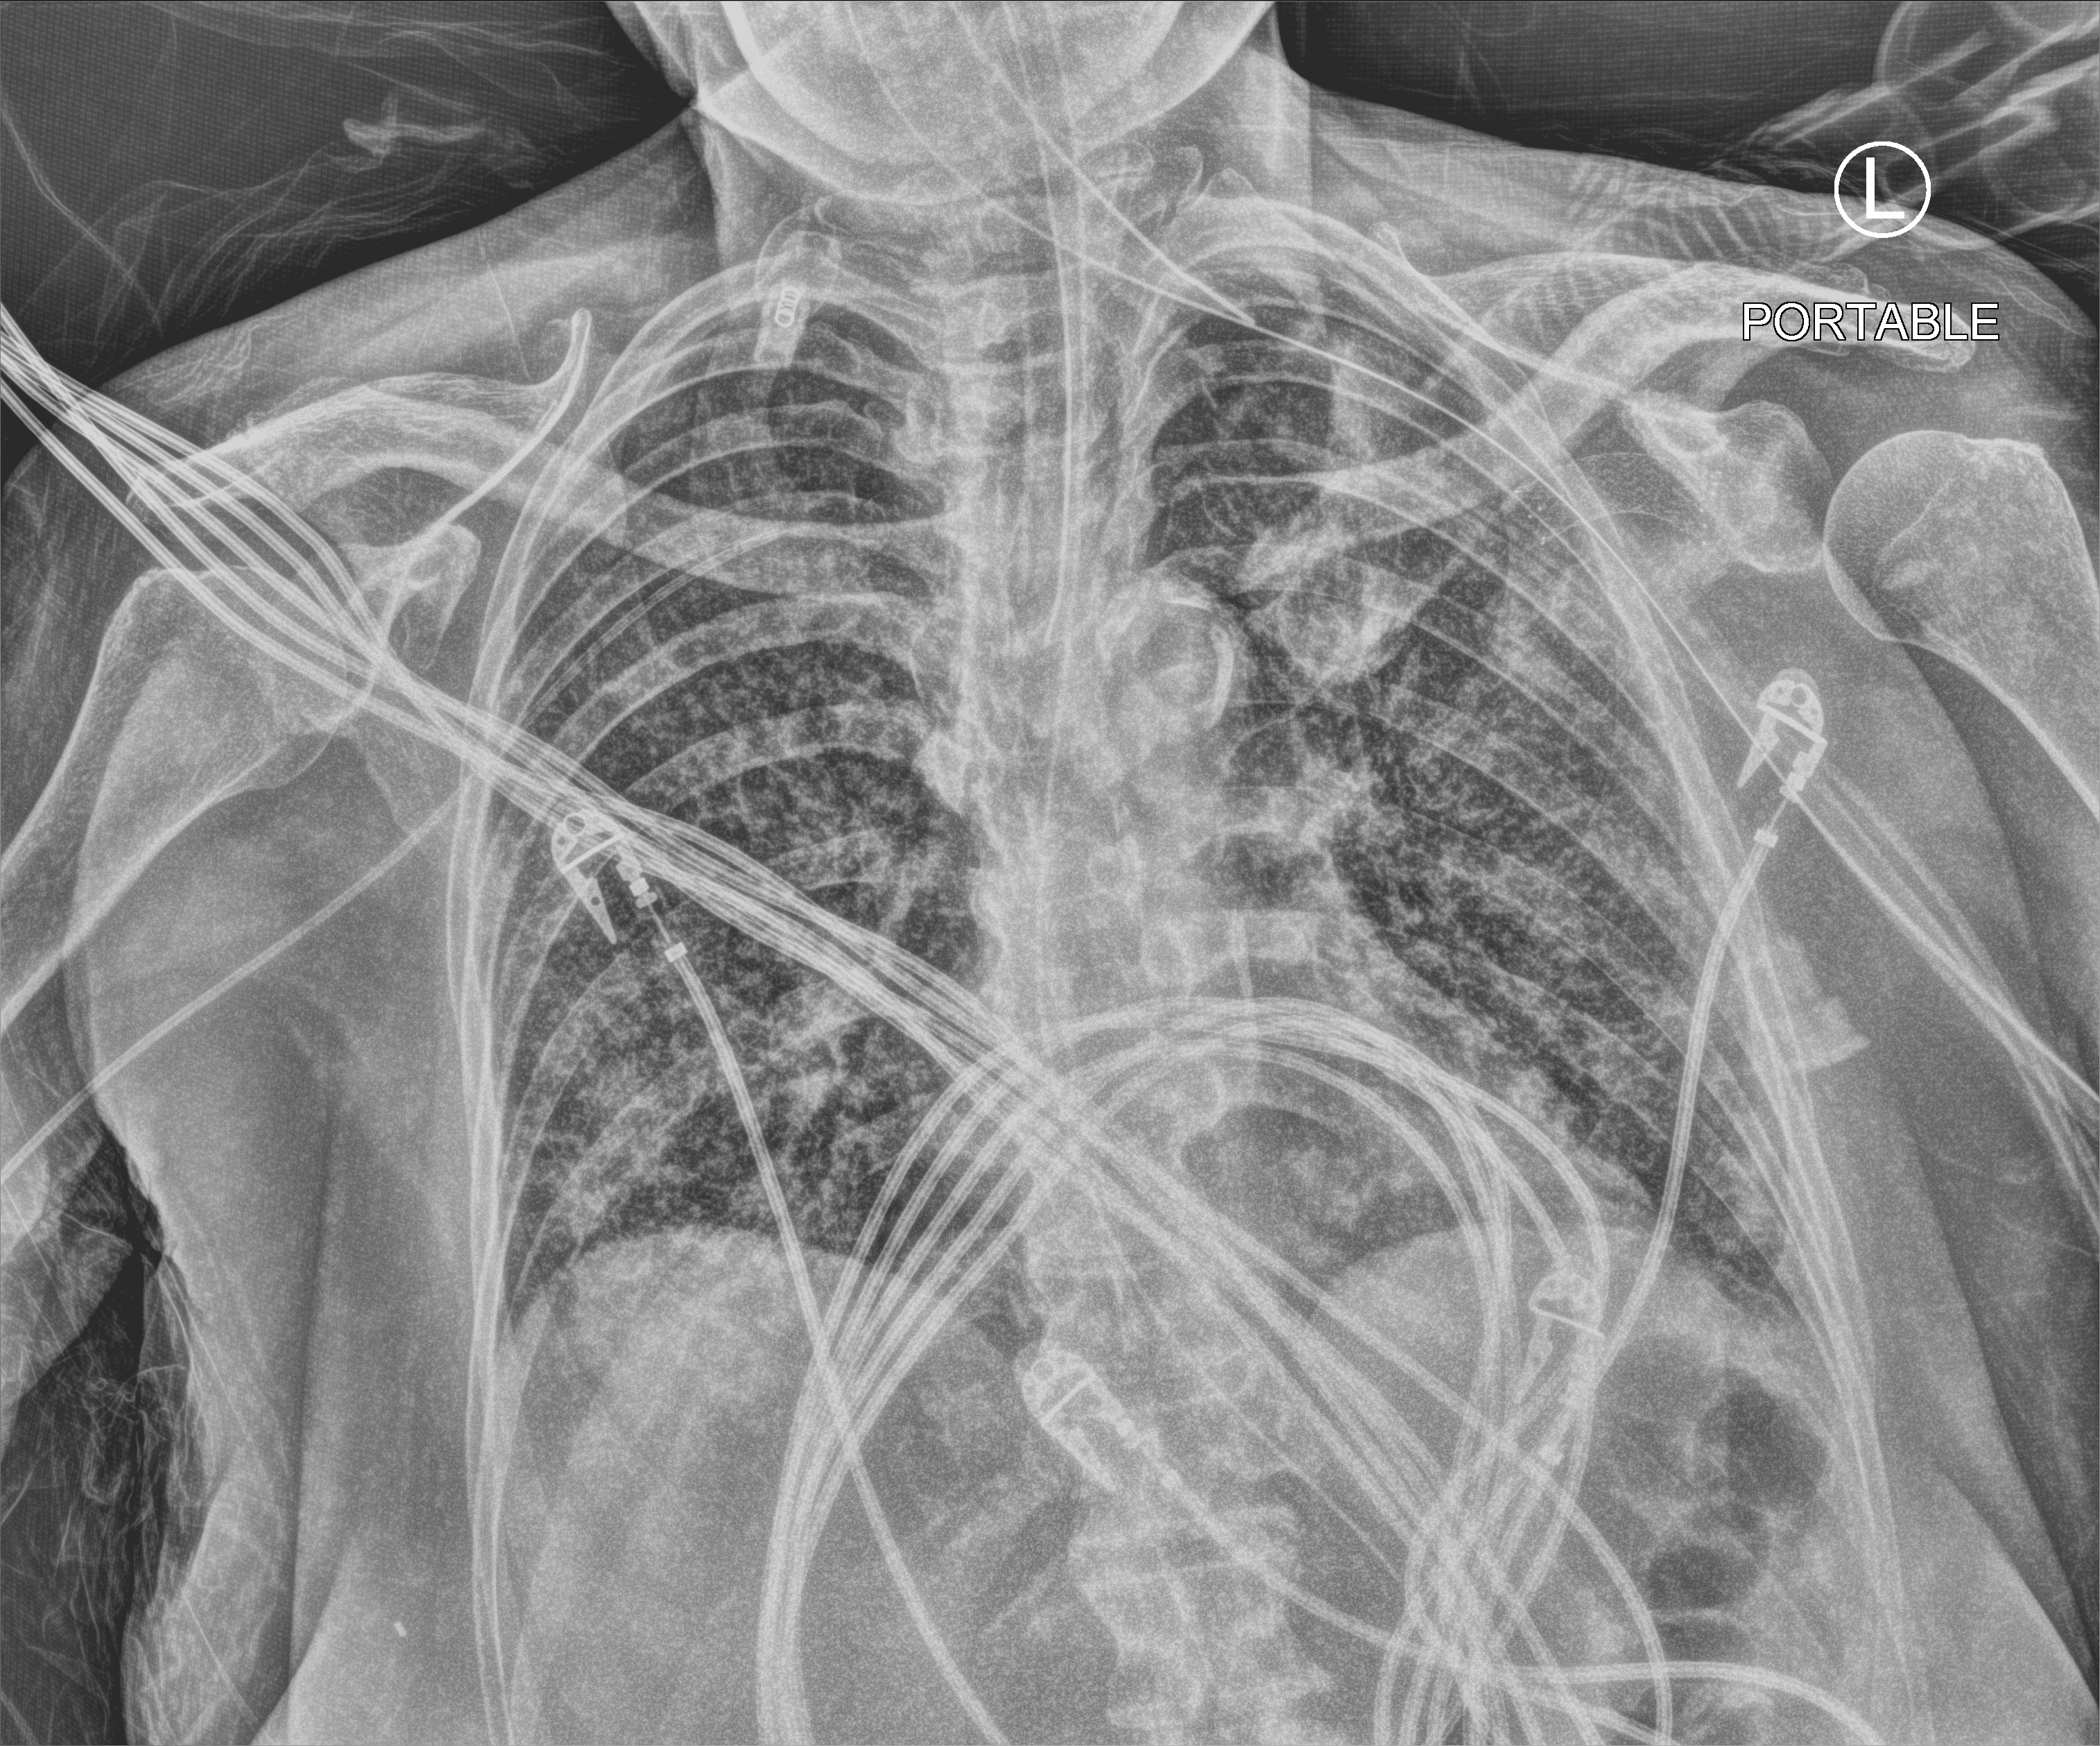
Bedside chest radiograph (computed radiography). Patient hospitalised with COVID-19; female, aged 60–74 years.
From the hospital-stay record, not from the radiograph (when in the stay this image was taken is not recorded): diabetes (admission record): yes; admitted to intensive care during this hospital stay: yes.